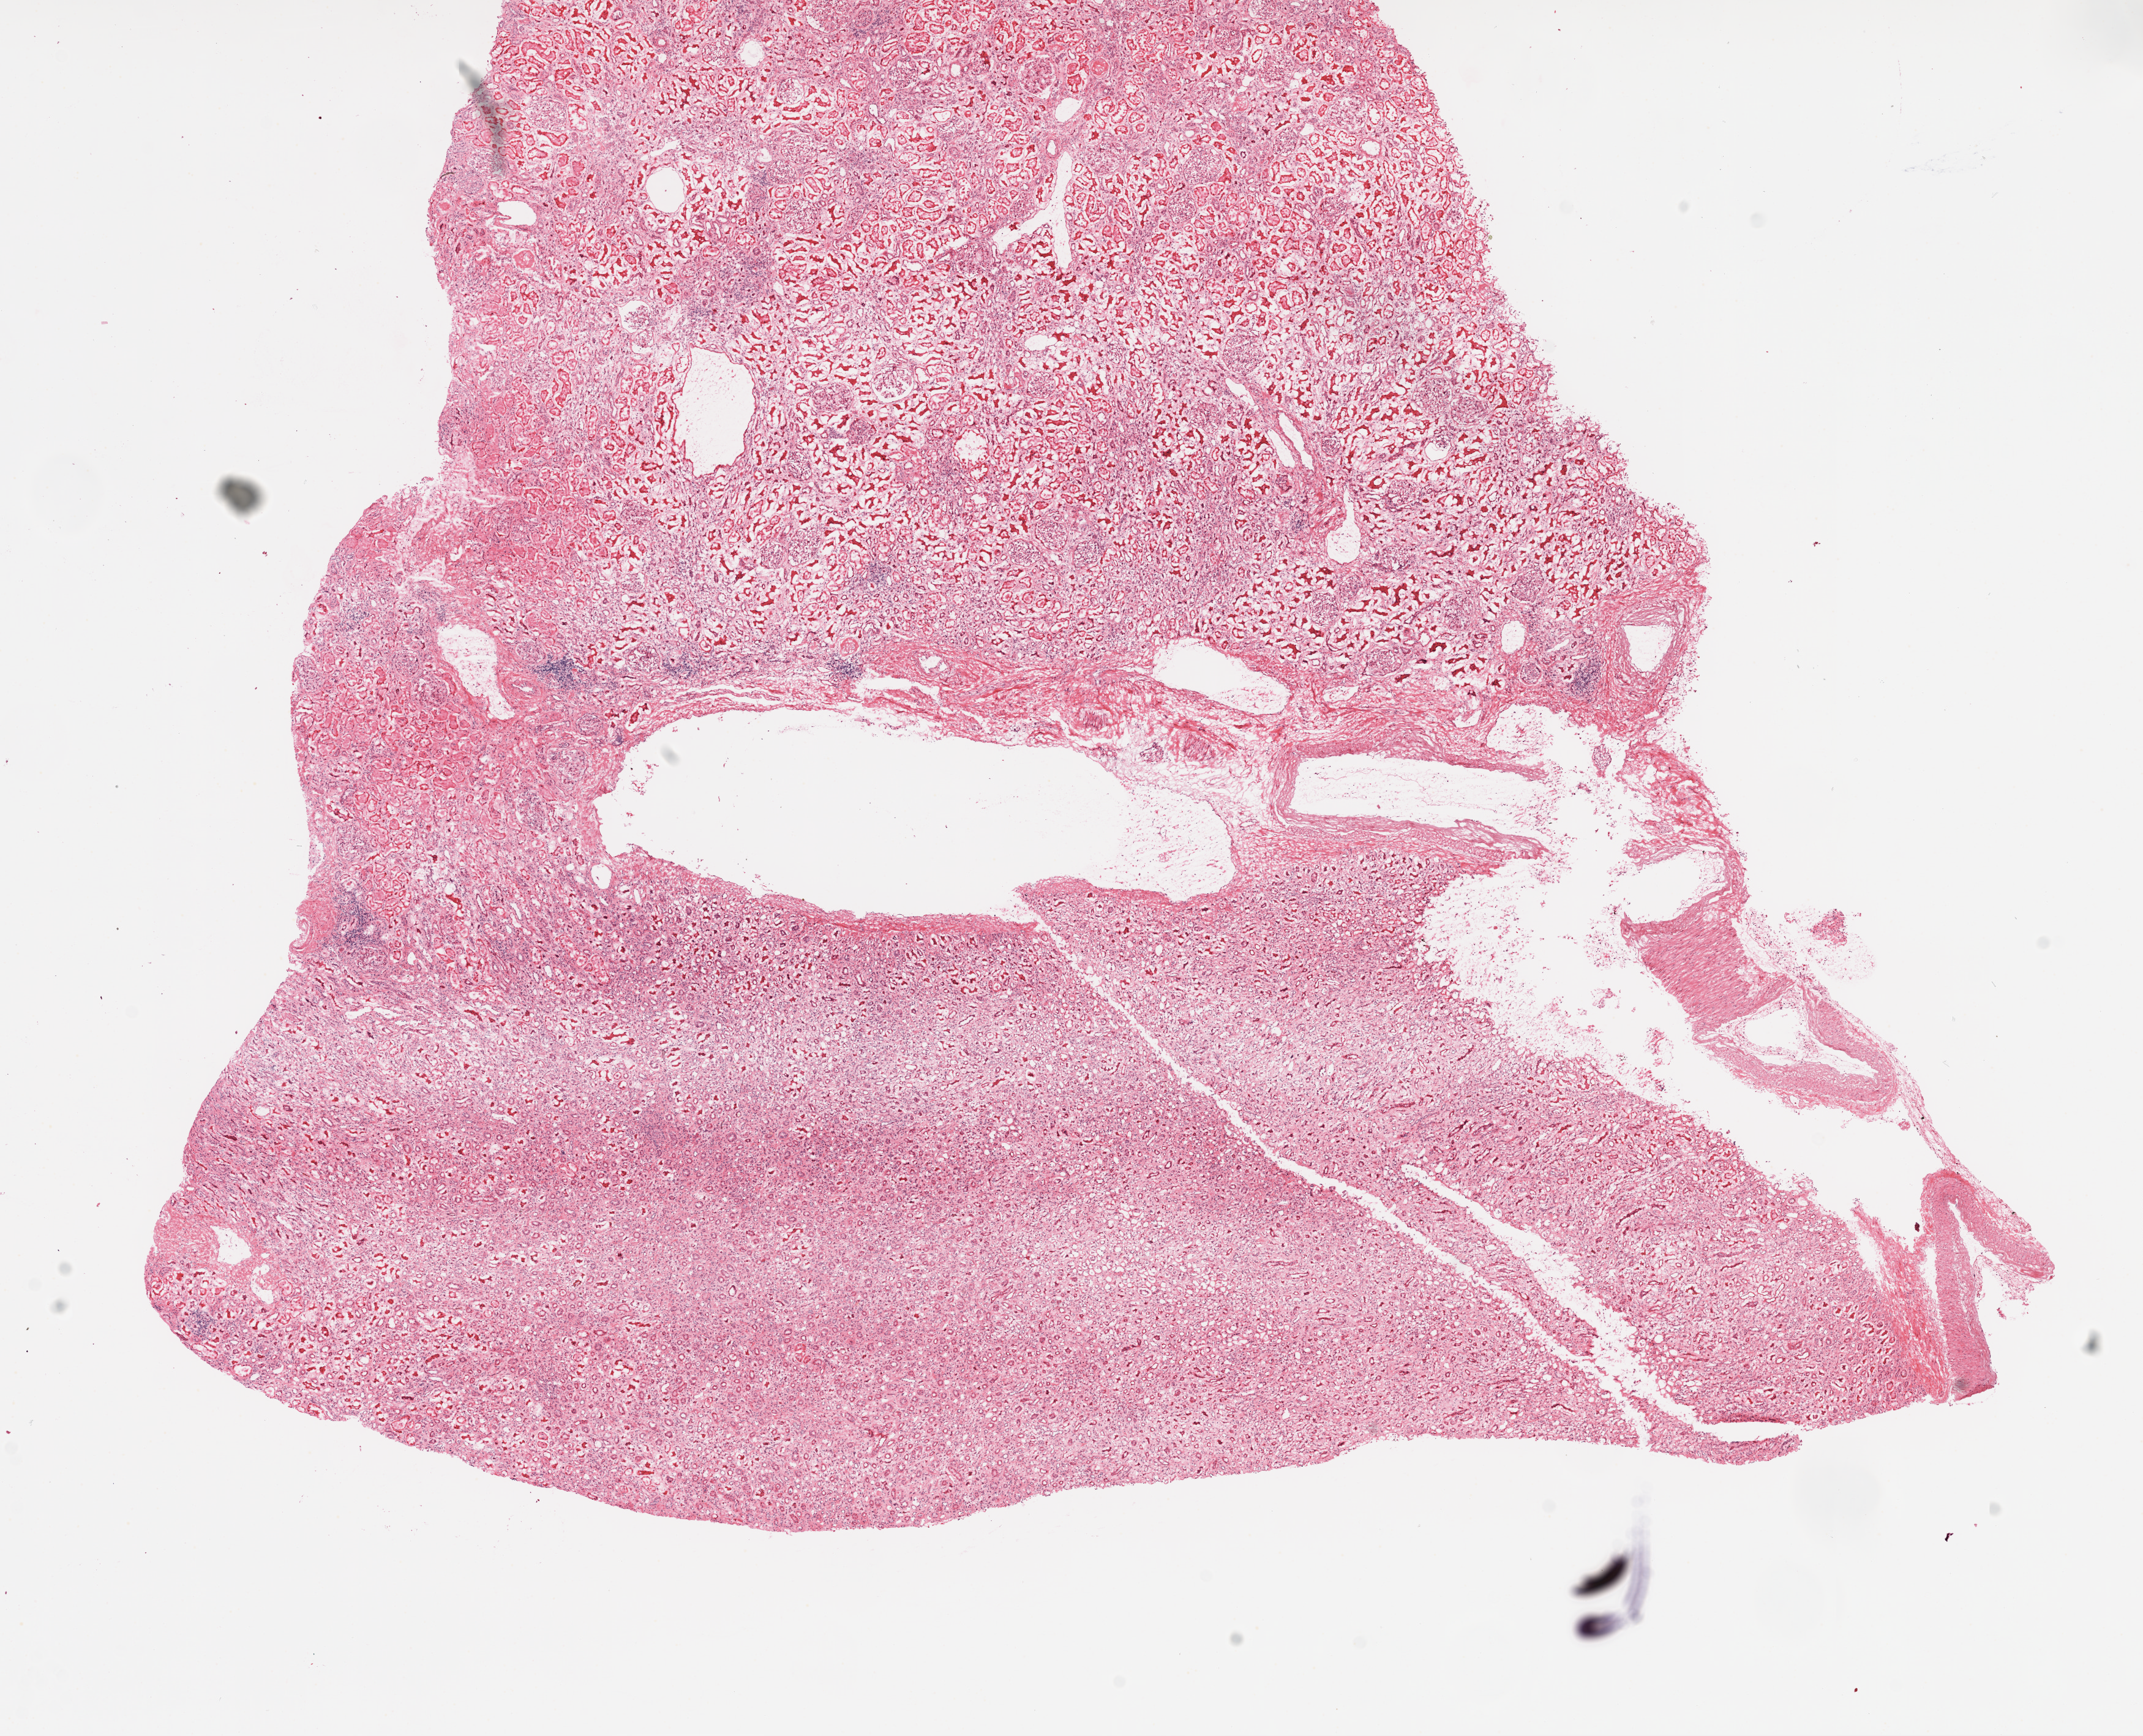
H&E-stained whole-slide image, low-resolution overview of the scanned area, about 14.0 x 11.4 mm (acquisition: 20x scan), frozen section from the top of the tissue portion, kidney, solid tissue normal (non-tumour tissue) sample. Male patient; age at initial diagnosis 67 years.
This section: solid tissue normal (non-tumour) sample from the same patient. Patient diagnosis: Clear cell adenocarcinoma, NOS.